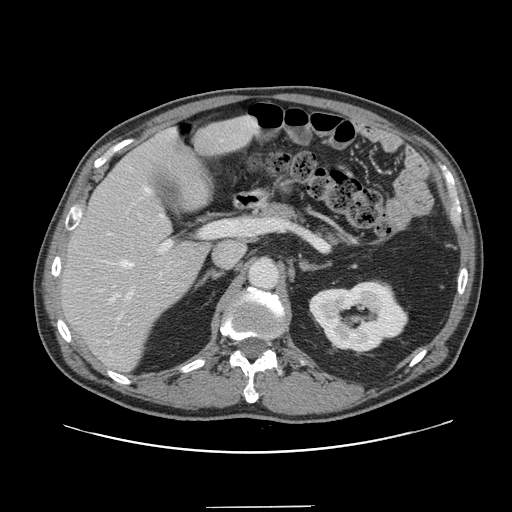
Contrast-enhanced abdominal CT, one axial slice; slice 86 of 139 in the series (ordered by position); 120 kVp; intravenous contrast given; soft-tissue window (W 400 / L 40 HU); 2.5 mm slice thickness; 512 × 512 image matrix, field of view 397 × 397 mm. Male patient, age 64 years. Case-level facts recorded for this patient, not image findings: diagnosis: colorectal cancer liver metastases, imaged before liver resection; multiple liver metastases: yes; largest metastasis: 3.5 cm; chemotherapy before resection: yes.
Annotated regions visible in this slice (outlined manually by an expert reader):
- hepatic veins: bounding box (x1, y1, x2, y2) in pixels: (110, 140, 222, 302)
- liver: (62, 117, 257, 370)
- planned liver remnant (the part of the liver to remain after resection): (62, 117, 256, 370)
- portal vein (with intrahepatic branches): (109, 223, 218, 320)